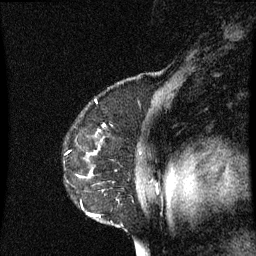
Breast MRI (dynamic contrast-enhanced), one sagittal slice; slice 53 of 60 in the series (ordered by position); dynamic contrast-enhanced series, image 2 of 3 at this slice position (ordered by acquisition); 1.5 T; TE 4.2 ms, TR 8.9 ms; 2 mm slice thickness; 256 × 256 image matrix, field of view 200 × 200 mm. Patient: female, 53 years. From the clinical record (not read from this slice): setting: breast cancer imaged before/during neoadjuvant chemotherapy; receptor status: HR-positive, HER2-negative.
Annotated regions visible in this slice (semi-automatic segmentation, software-assisted and operator-edited):
- analysis volume of interest (the breast-tissue region the enhancement analysis was run in; not a lesion): bounding box <78,148,155,229> (left, top, right, bottom; pixels)
- tumour enhancement mask (voxels above the 70 % enhancement threshold inside the analysis volume of interest): <88,152,97,217>